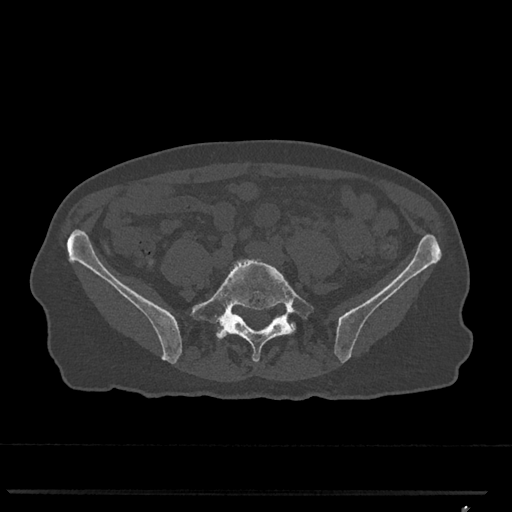
CT including the spine, one axial slice; position 150 of 793 along the scan axis; bone window (W 1800 / L 400 HU); 0.5 mm slice thickness; 512 × 512 image matrix, field of view 380 × 380 mm. Patient: female, 62 years. From the clinical record (not read from this slice): primary cancer: renal.
Outlined on this slice (semi-automatic segmentation, software-assisted and operator-edited):
- L5 vertebra: bounding box (x1, y1, x2, y2) in pixels: (190, 259, 314, 362)